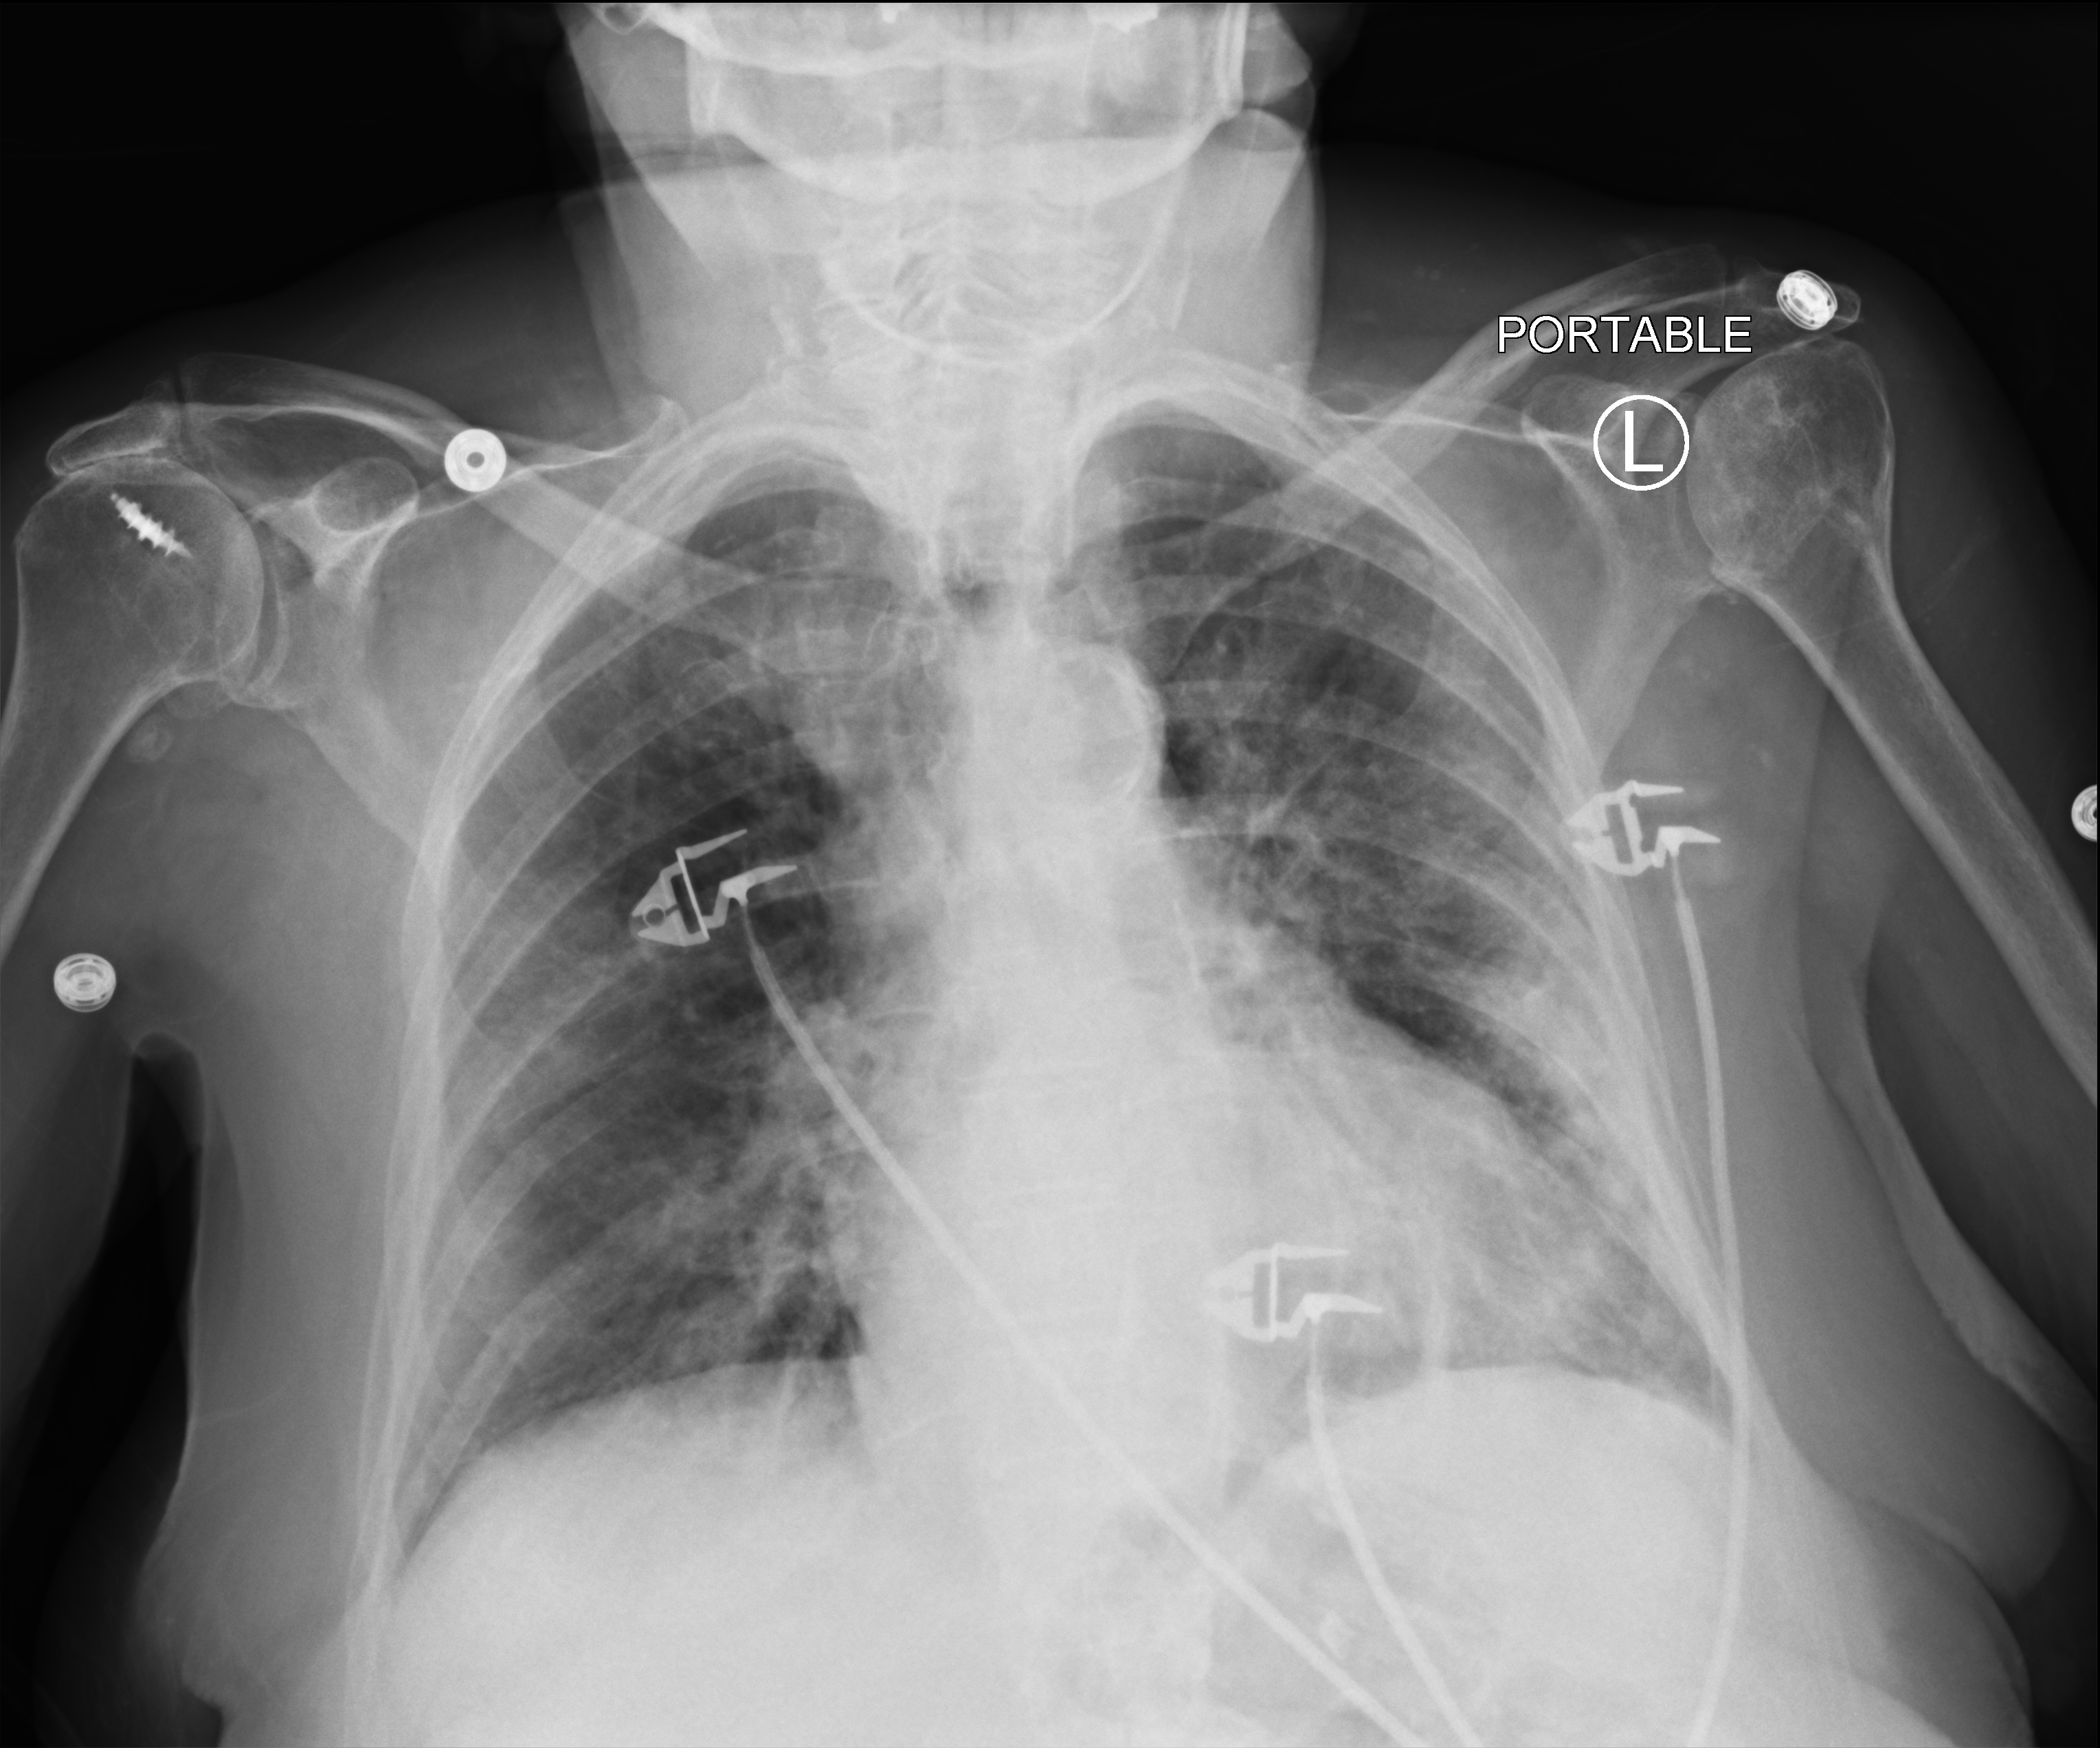
Portable chest radiograph, anteroposterior (AP) projection. Patient hospitalised with COVID-19; female, aged 75–90 years.
From the hospital-stay record, not from the radiograph (when in the stay this image was taken is not recorded):
- length of hospital stay: 13 days
- mechanically ventilated during this hospital stay: no